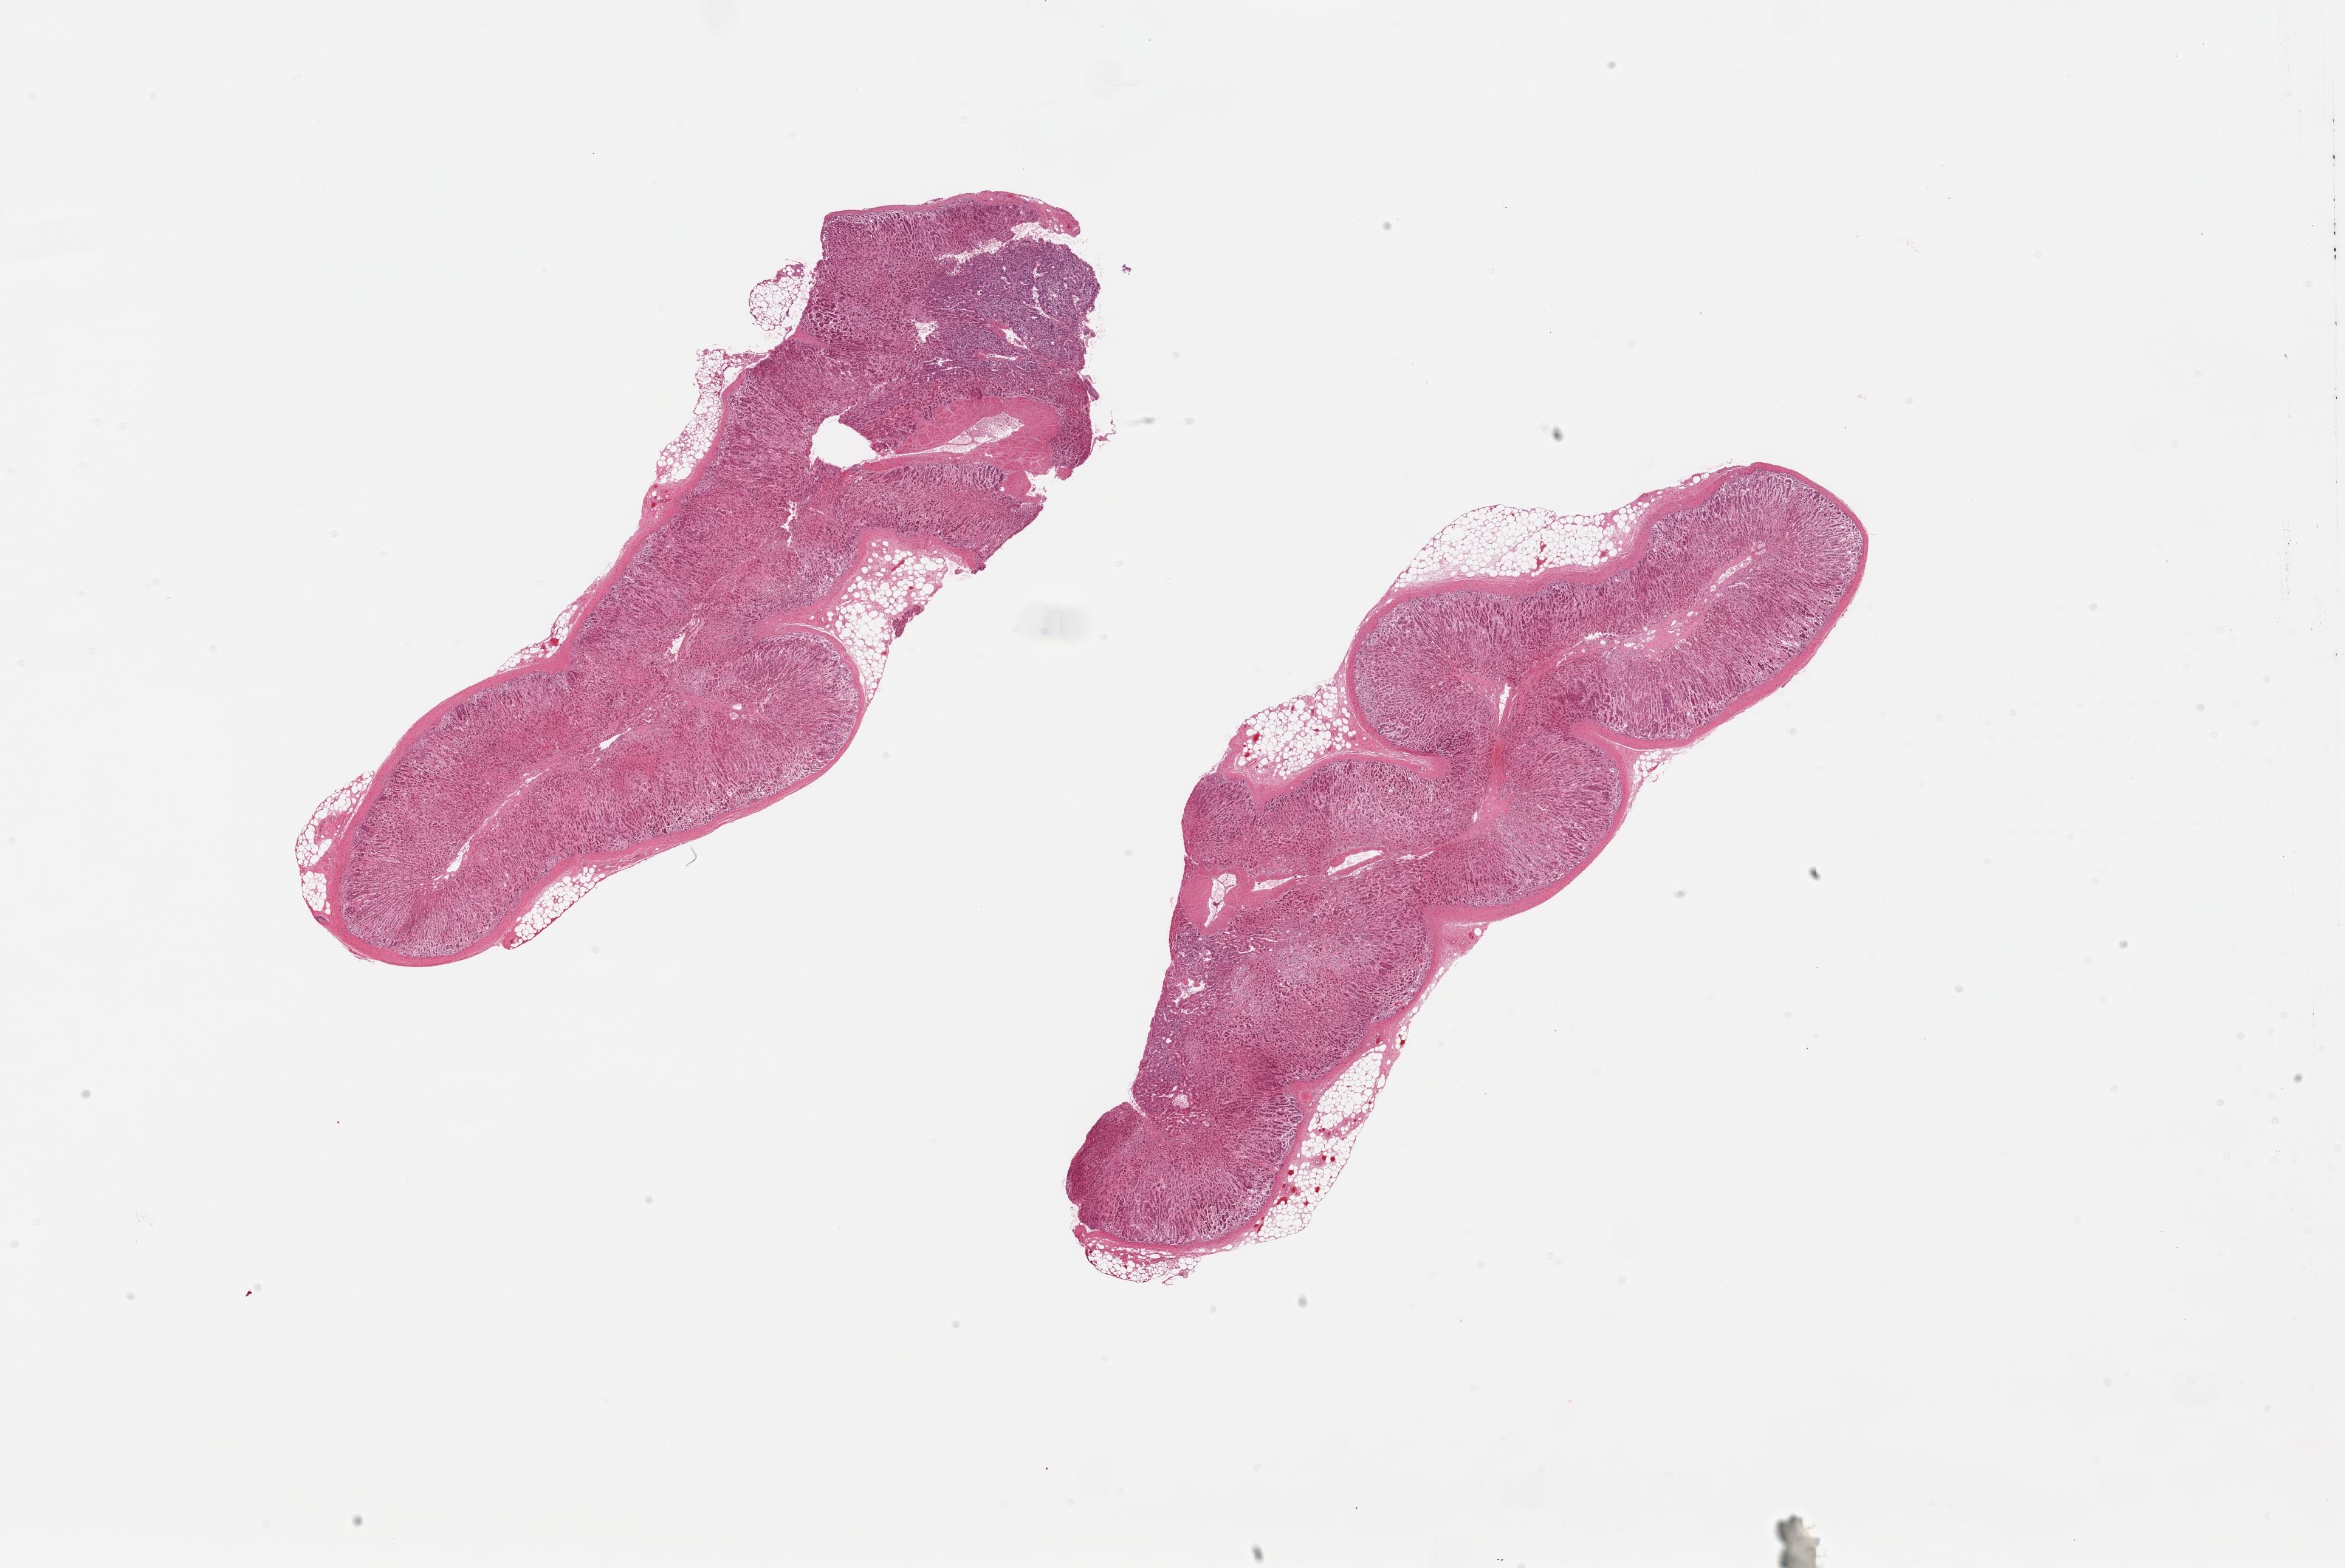
Hematoxylin and eosin (H&E) whole-slide image, whole scanned area (about 30.5 x 20.4 mm) shown as a low-resolution overview; PAXgene-fixed paraffin-embedded (PFPE) section; section of adrenal gland (target tissue); tissue donor sample. Male donor.
Pathologist's review note for this sample: 2 pieces; 10% external fat.